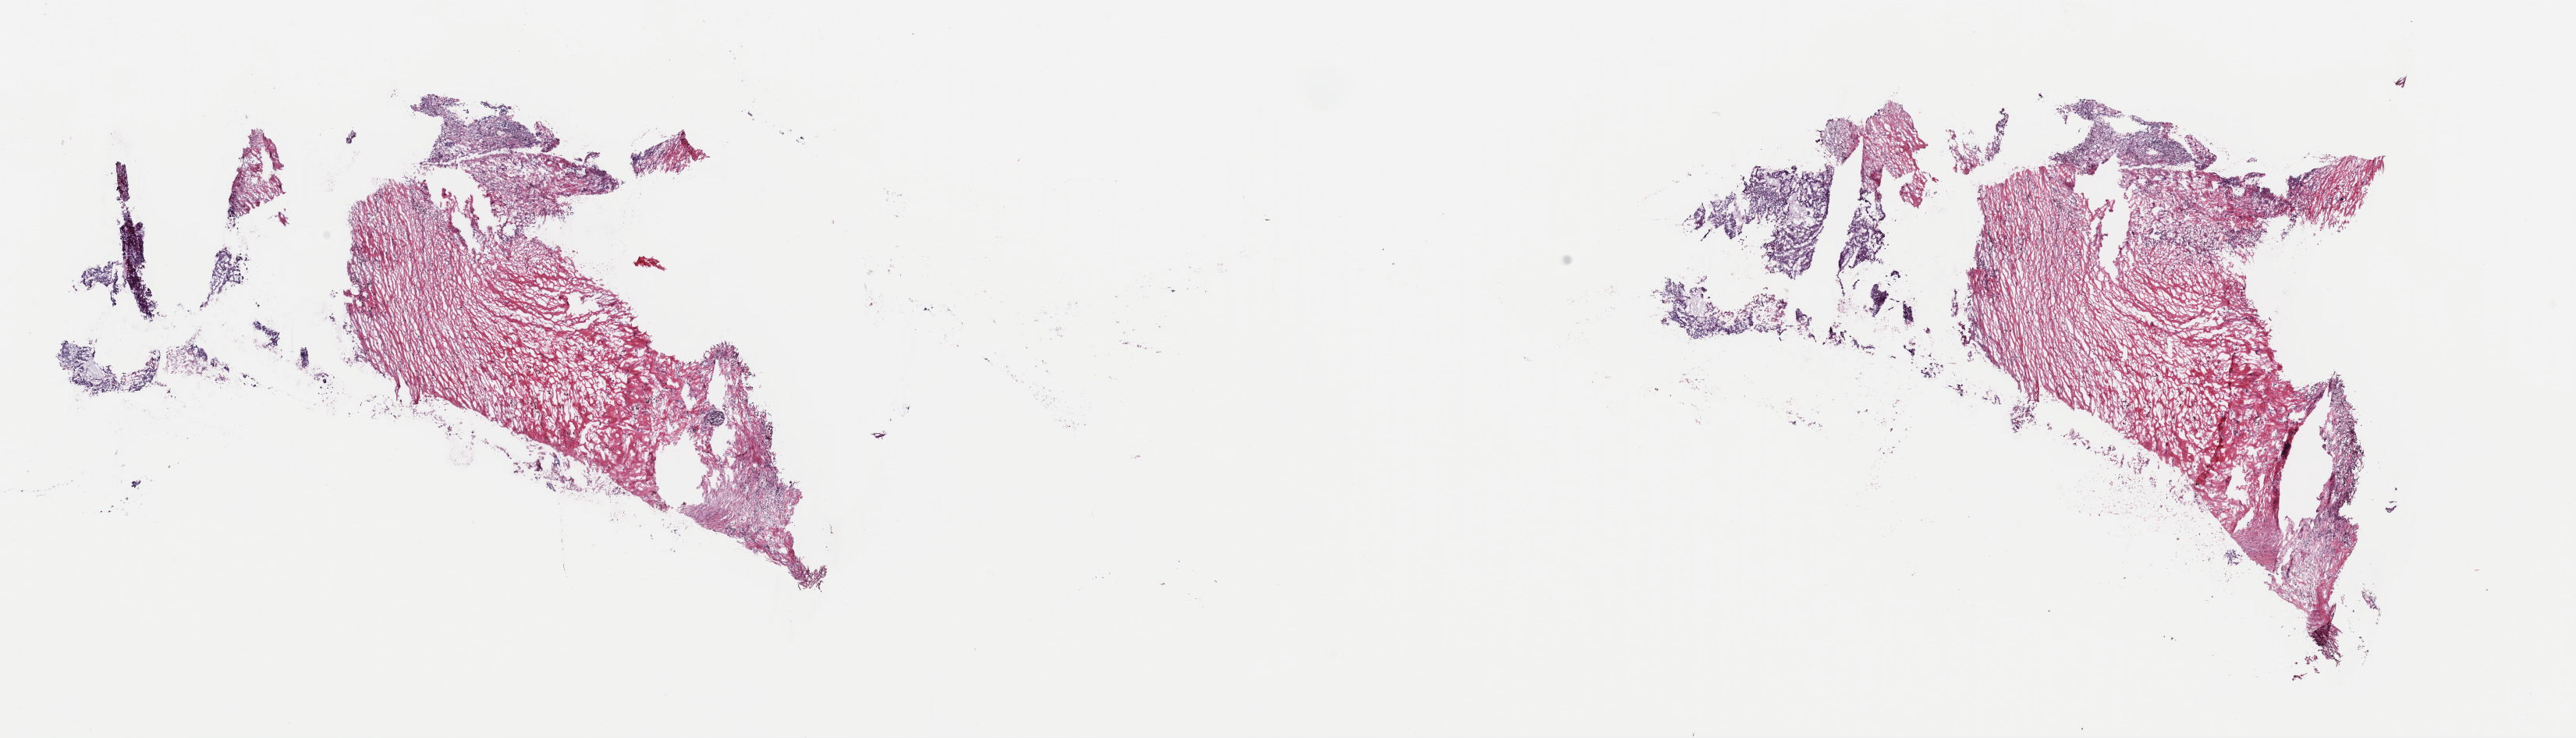
H&E-stained whole-slide image, low-resolution overview of the scanned area, about 26.1 x 7.5 mm; frozen section; primary tumour sample from the kidney. Male patient; age at initial diagnosis 64 years. Composition of this section per pathologist review: tumour cells 60%, tumour nuclei 60%, normal cells 0%, stromal cells 40%, necrosis 0%. Infiltration values recorded for this section: lymphocyte infiltration 10%, monocyte infiltration 5%, neutrophil infiltration 0%.
Laterality: left. AJCC pathologic stage: I (7th edition). Histologic diagnosis: Papillary adenocarcinoma, NOS.